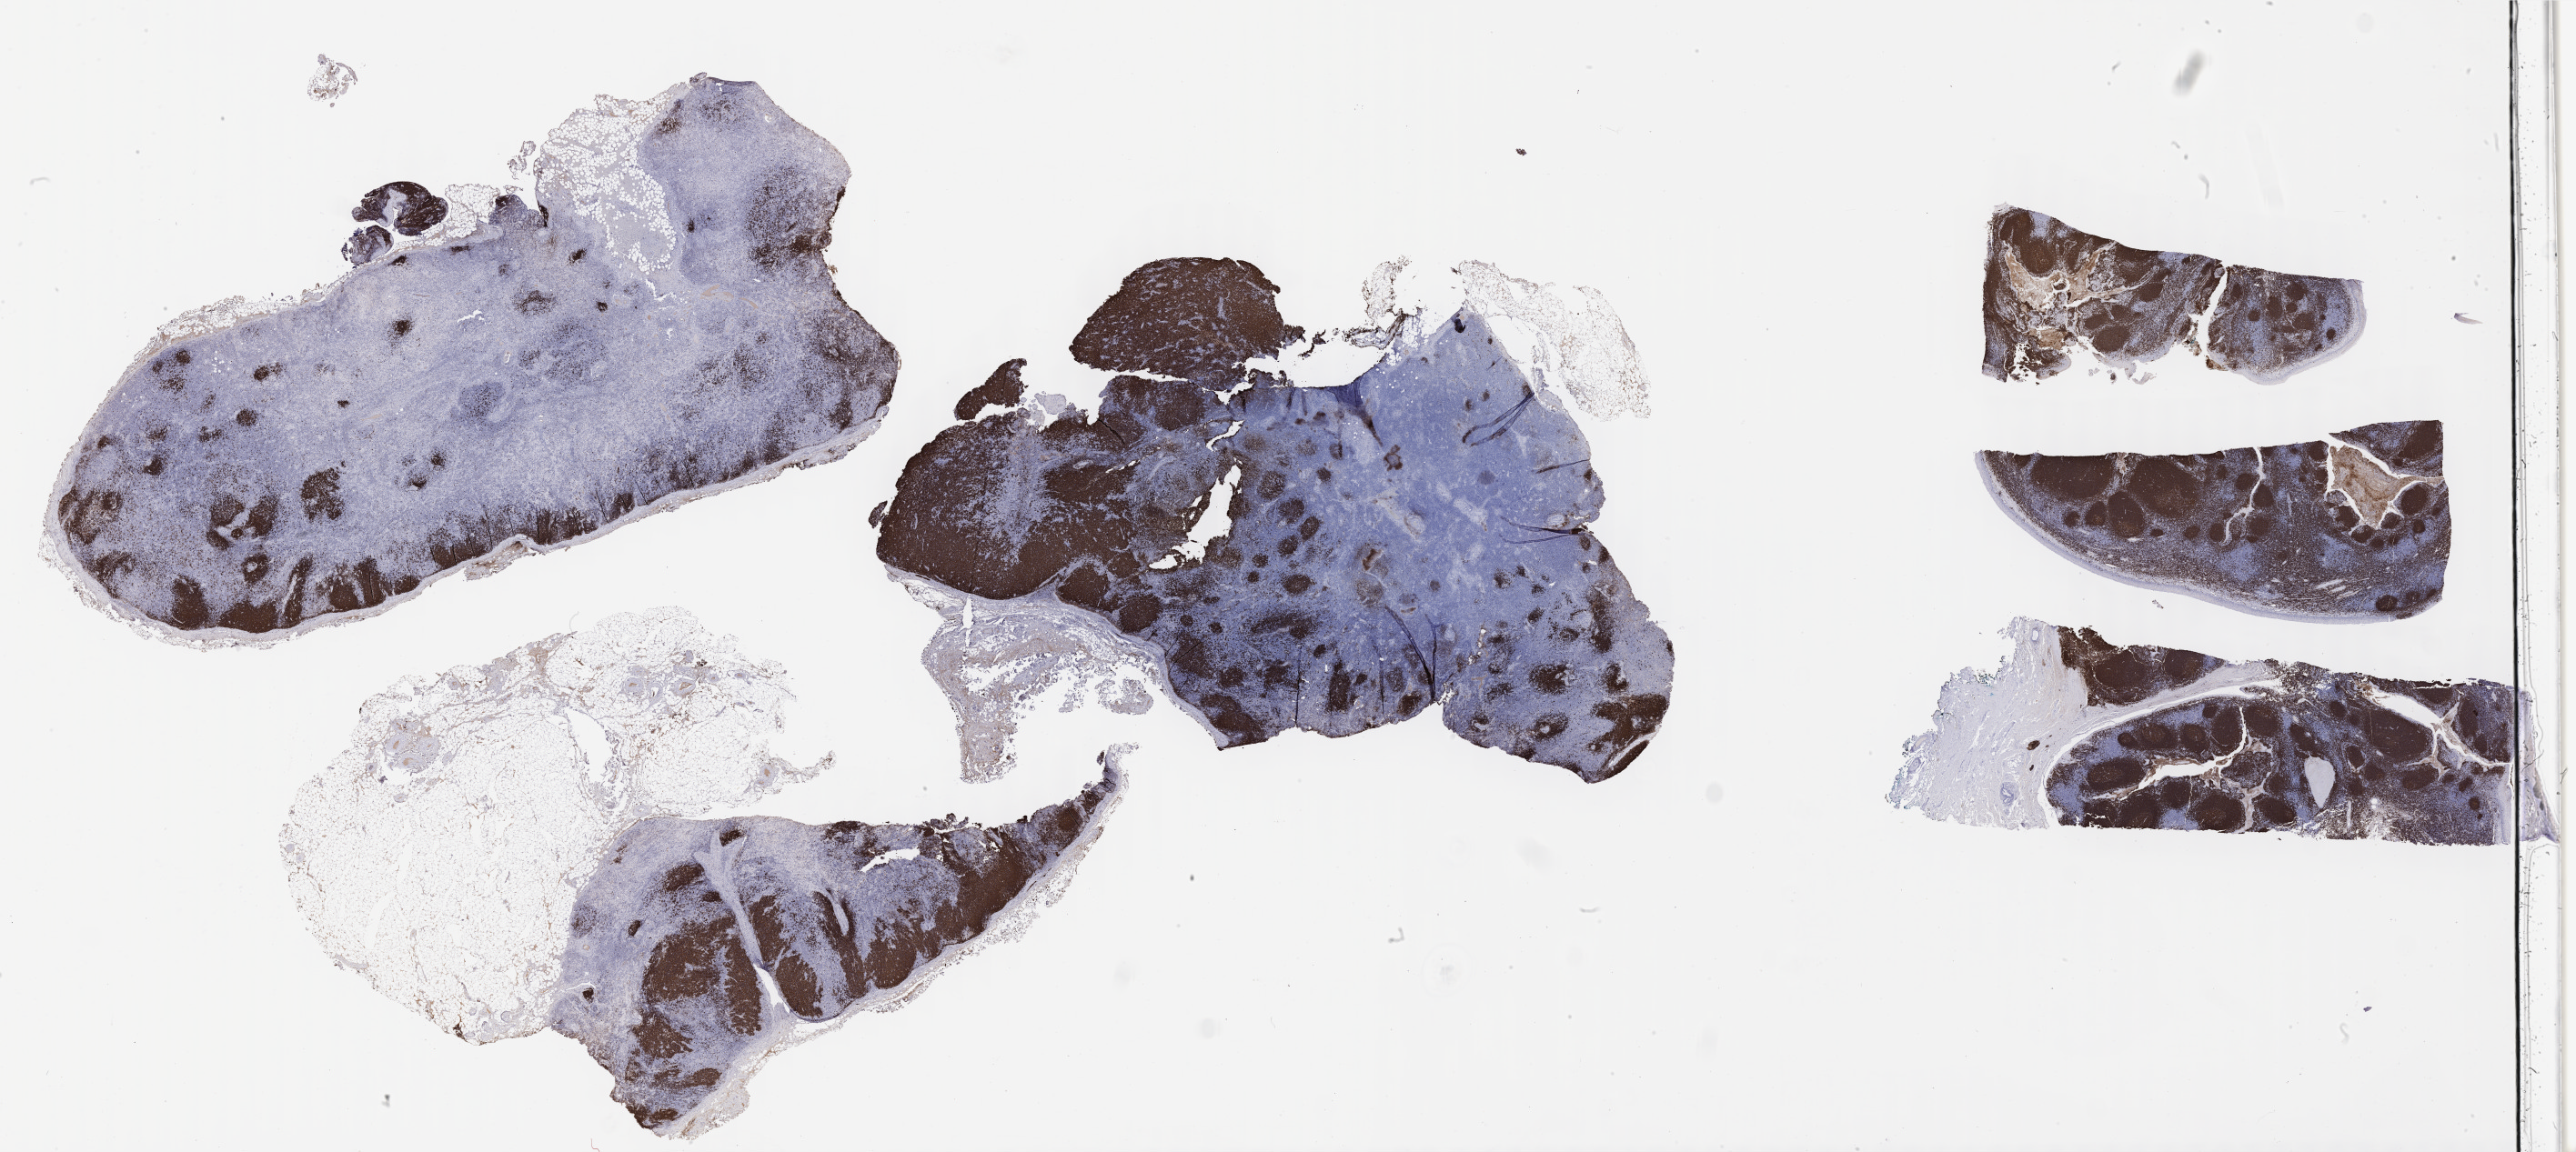
Immunohistochemistry (IHC) whole-slide image stained for CD20, whole scanned area (about 45.8 x 20.5 mm) shown as a low-resolution overview; tumor tissue; anatomic site: lymph node. Patient: male, aged 56.
• diagnosis: Diffuse large B-cell lymphoma, NOS